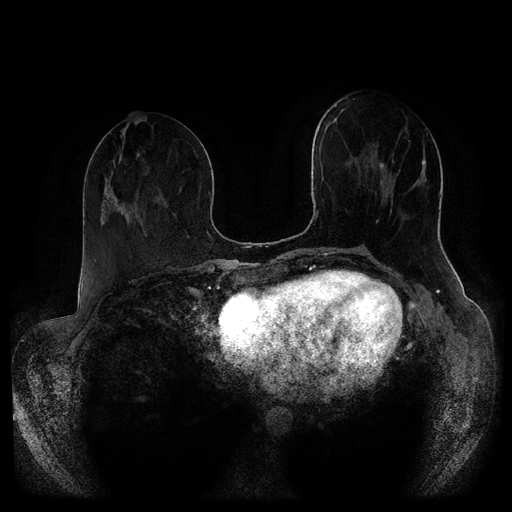
Breast MRI (dynamic contrast-enhanced, multi-phase), one axial slice; position 37 of 116 along the scan axis; dynamic contrast-enhanced series, time point 2 of 5 at this slice position (early post-contrast); 1.5 T; TE 2.6 ms, TR 5.3 ms; 512 × 512 image matrix, field of view 370 × 370 mm. Patient: female, 51 years.
Outlined on this slice (semi-automatic segmentation, software-assisted and operator-edited):
- breast lesion (labelled 'tumour' in the annotation; benign lesions carry a separate 'benign' label): bounding box <380,163,385,170> (left, top, right, bottom; pixels)